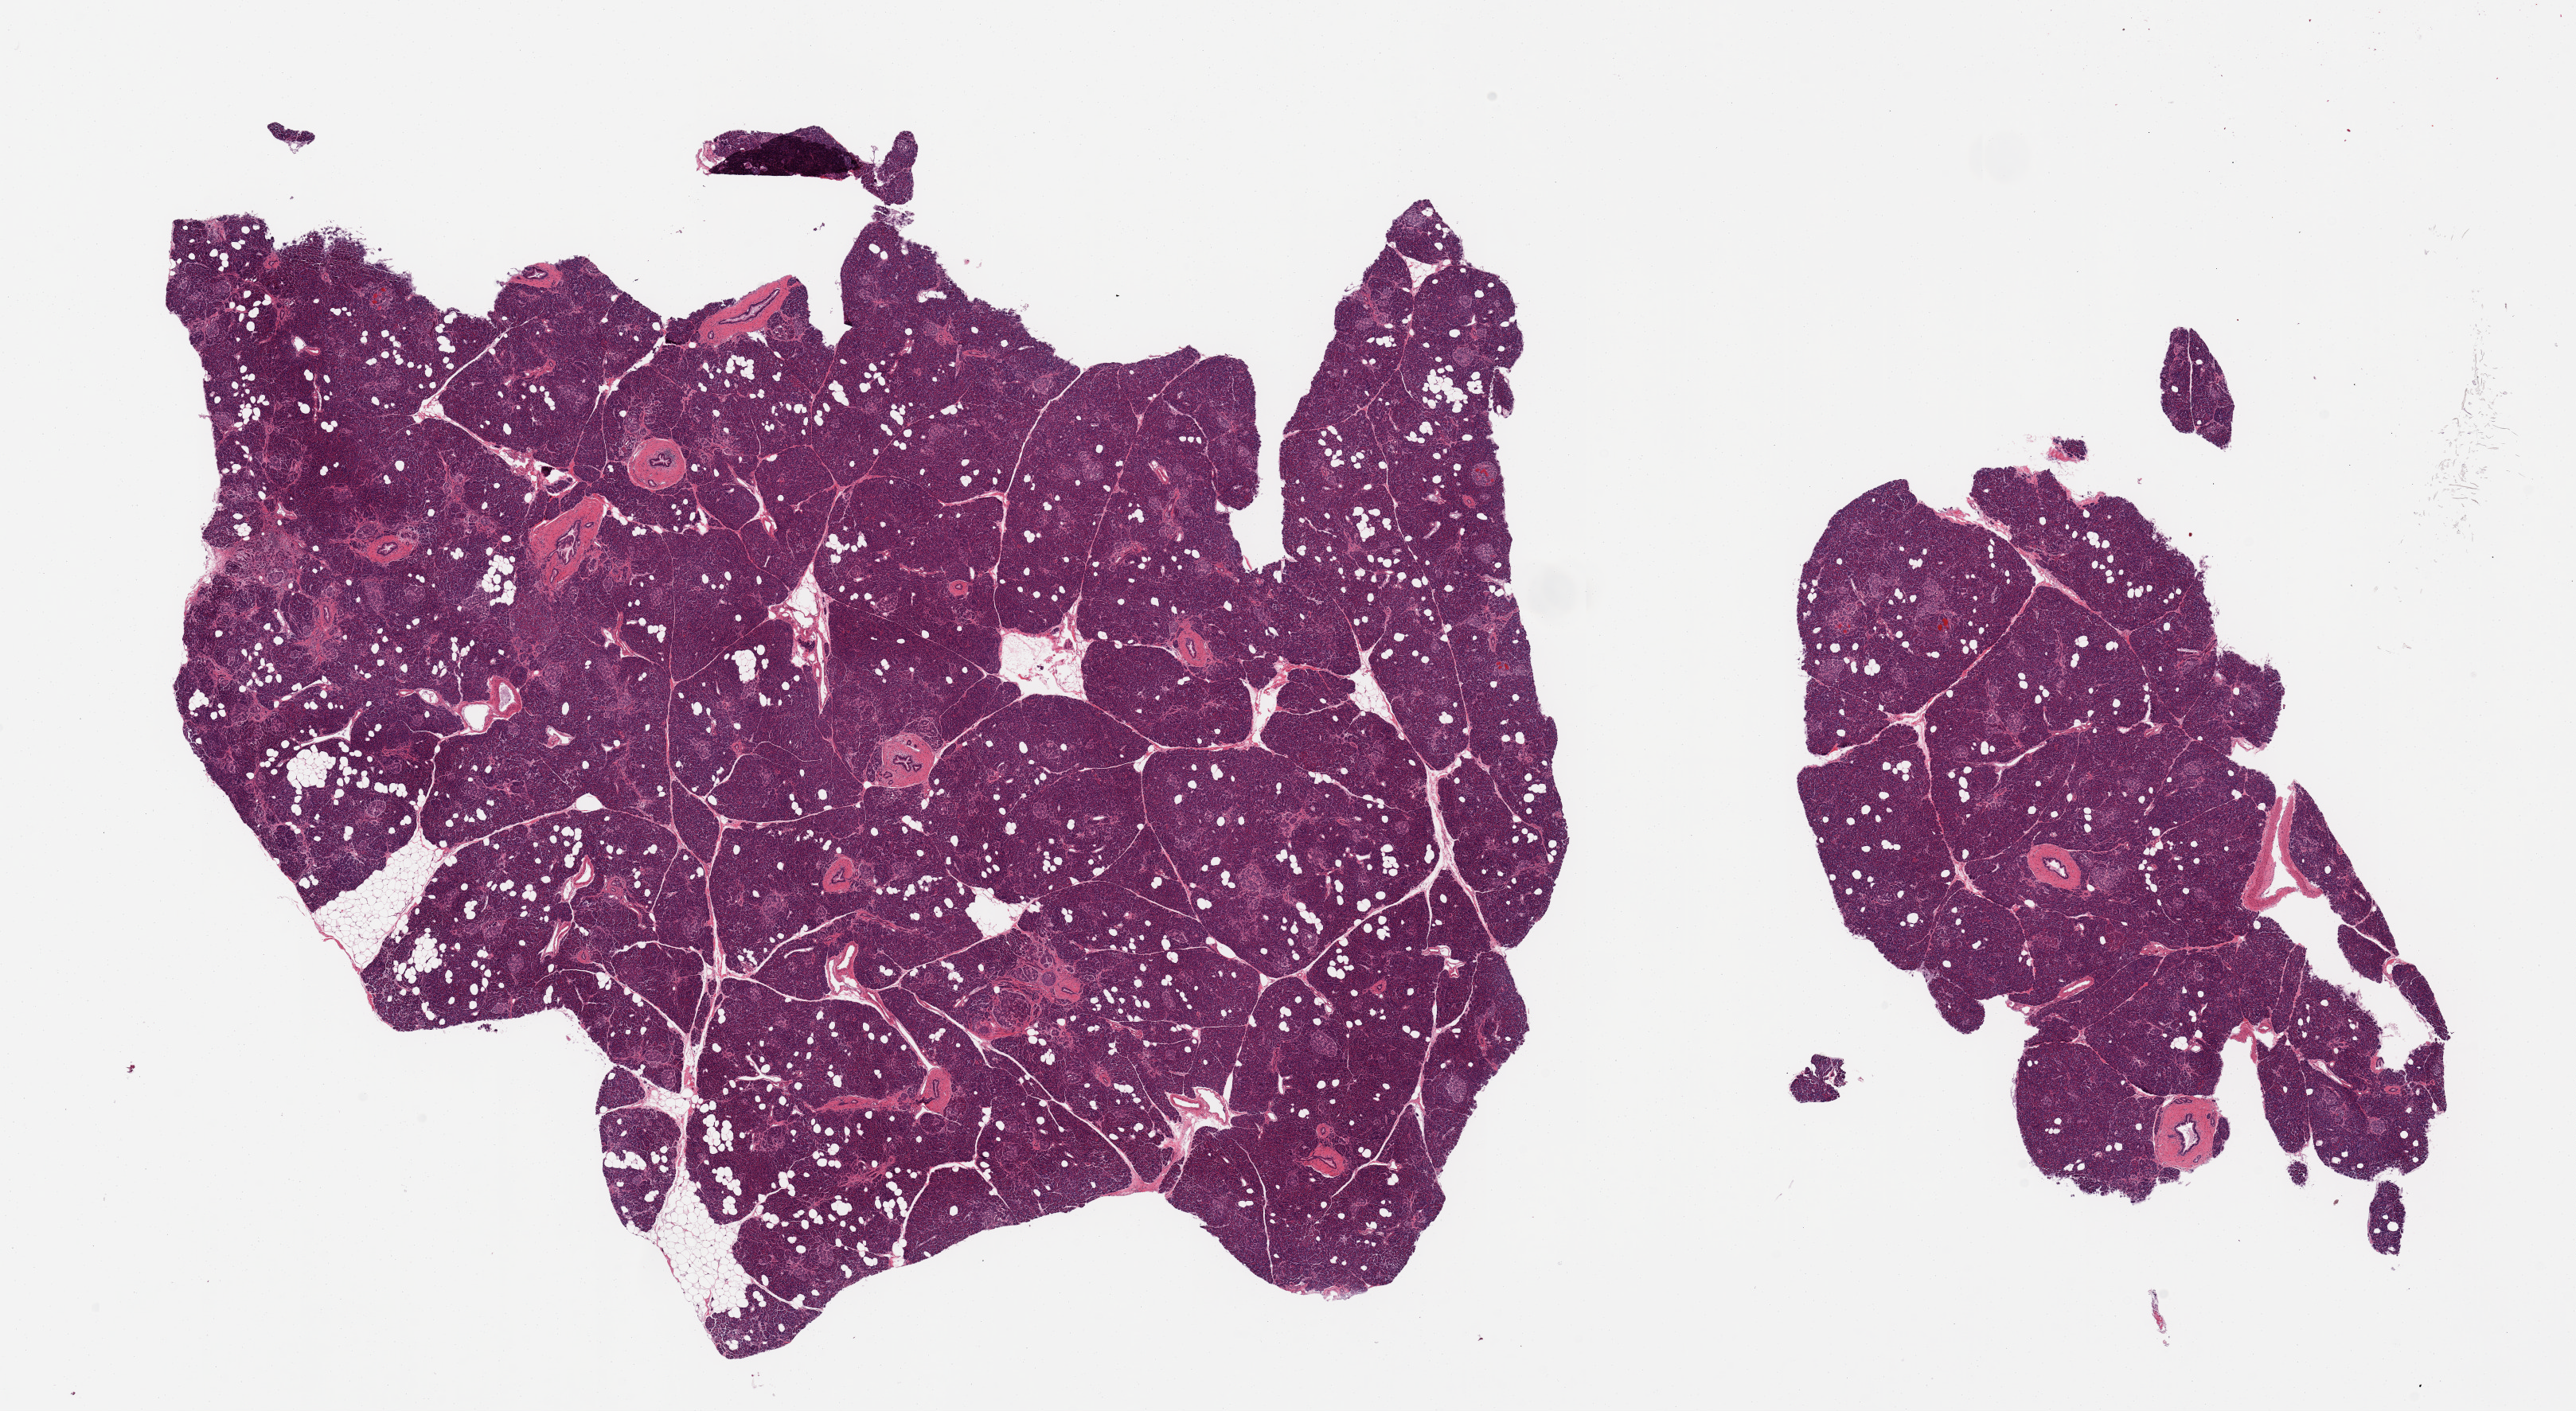
Digitized hematoxylin and eosin (H&E)-stained section — shown as a low-resolution overview of the whole scanned area (about 25.6 x 14.0 mm), PAXgene-fixed paraffin-embedded (PFPE) section, target tissue: pancreas, tissue donor sample. Donor: male.
* reviewer comment on this tissue sample: 2 pieces; abundant islets; 10% internal fat content as individual cells